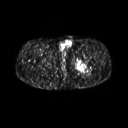
FDG PET of an extremity soft-tissue mass (from a PET/CT study), one axial slice; slice 258 of 267 in the series (ordered by position); 3.27 mm slice thickness; 128 × 128 image matrix, field of view 500 × 500 mm. Male patient, age 27 years. From the clinical record (not read from this slice): histological type: extraskeletal osteosarcoma; grade: high; site of the primary tumour: left adductur.
Outlined on this slice (expert contour drawn on MRI and transferred to this co-registered scan by the dataset authors):
- gross tumour volume (mass): bounding box [x1, y1, x2, y2] px = [72, 52, 95, 76]